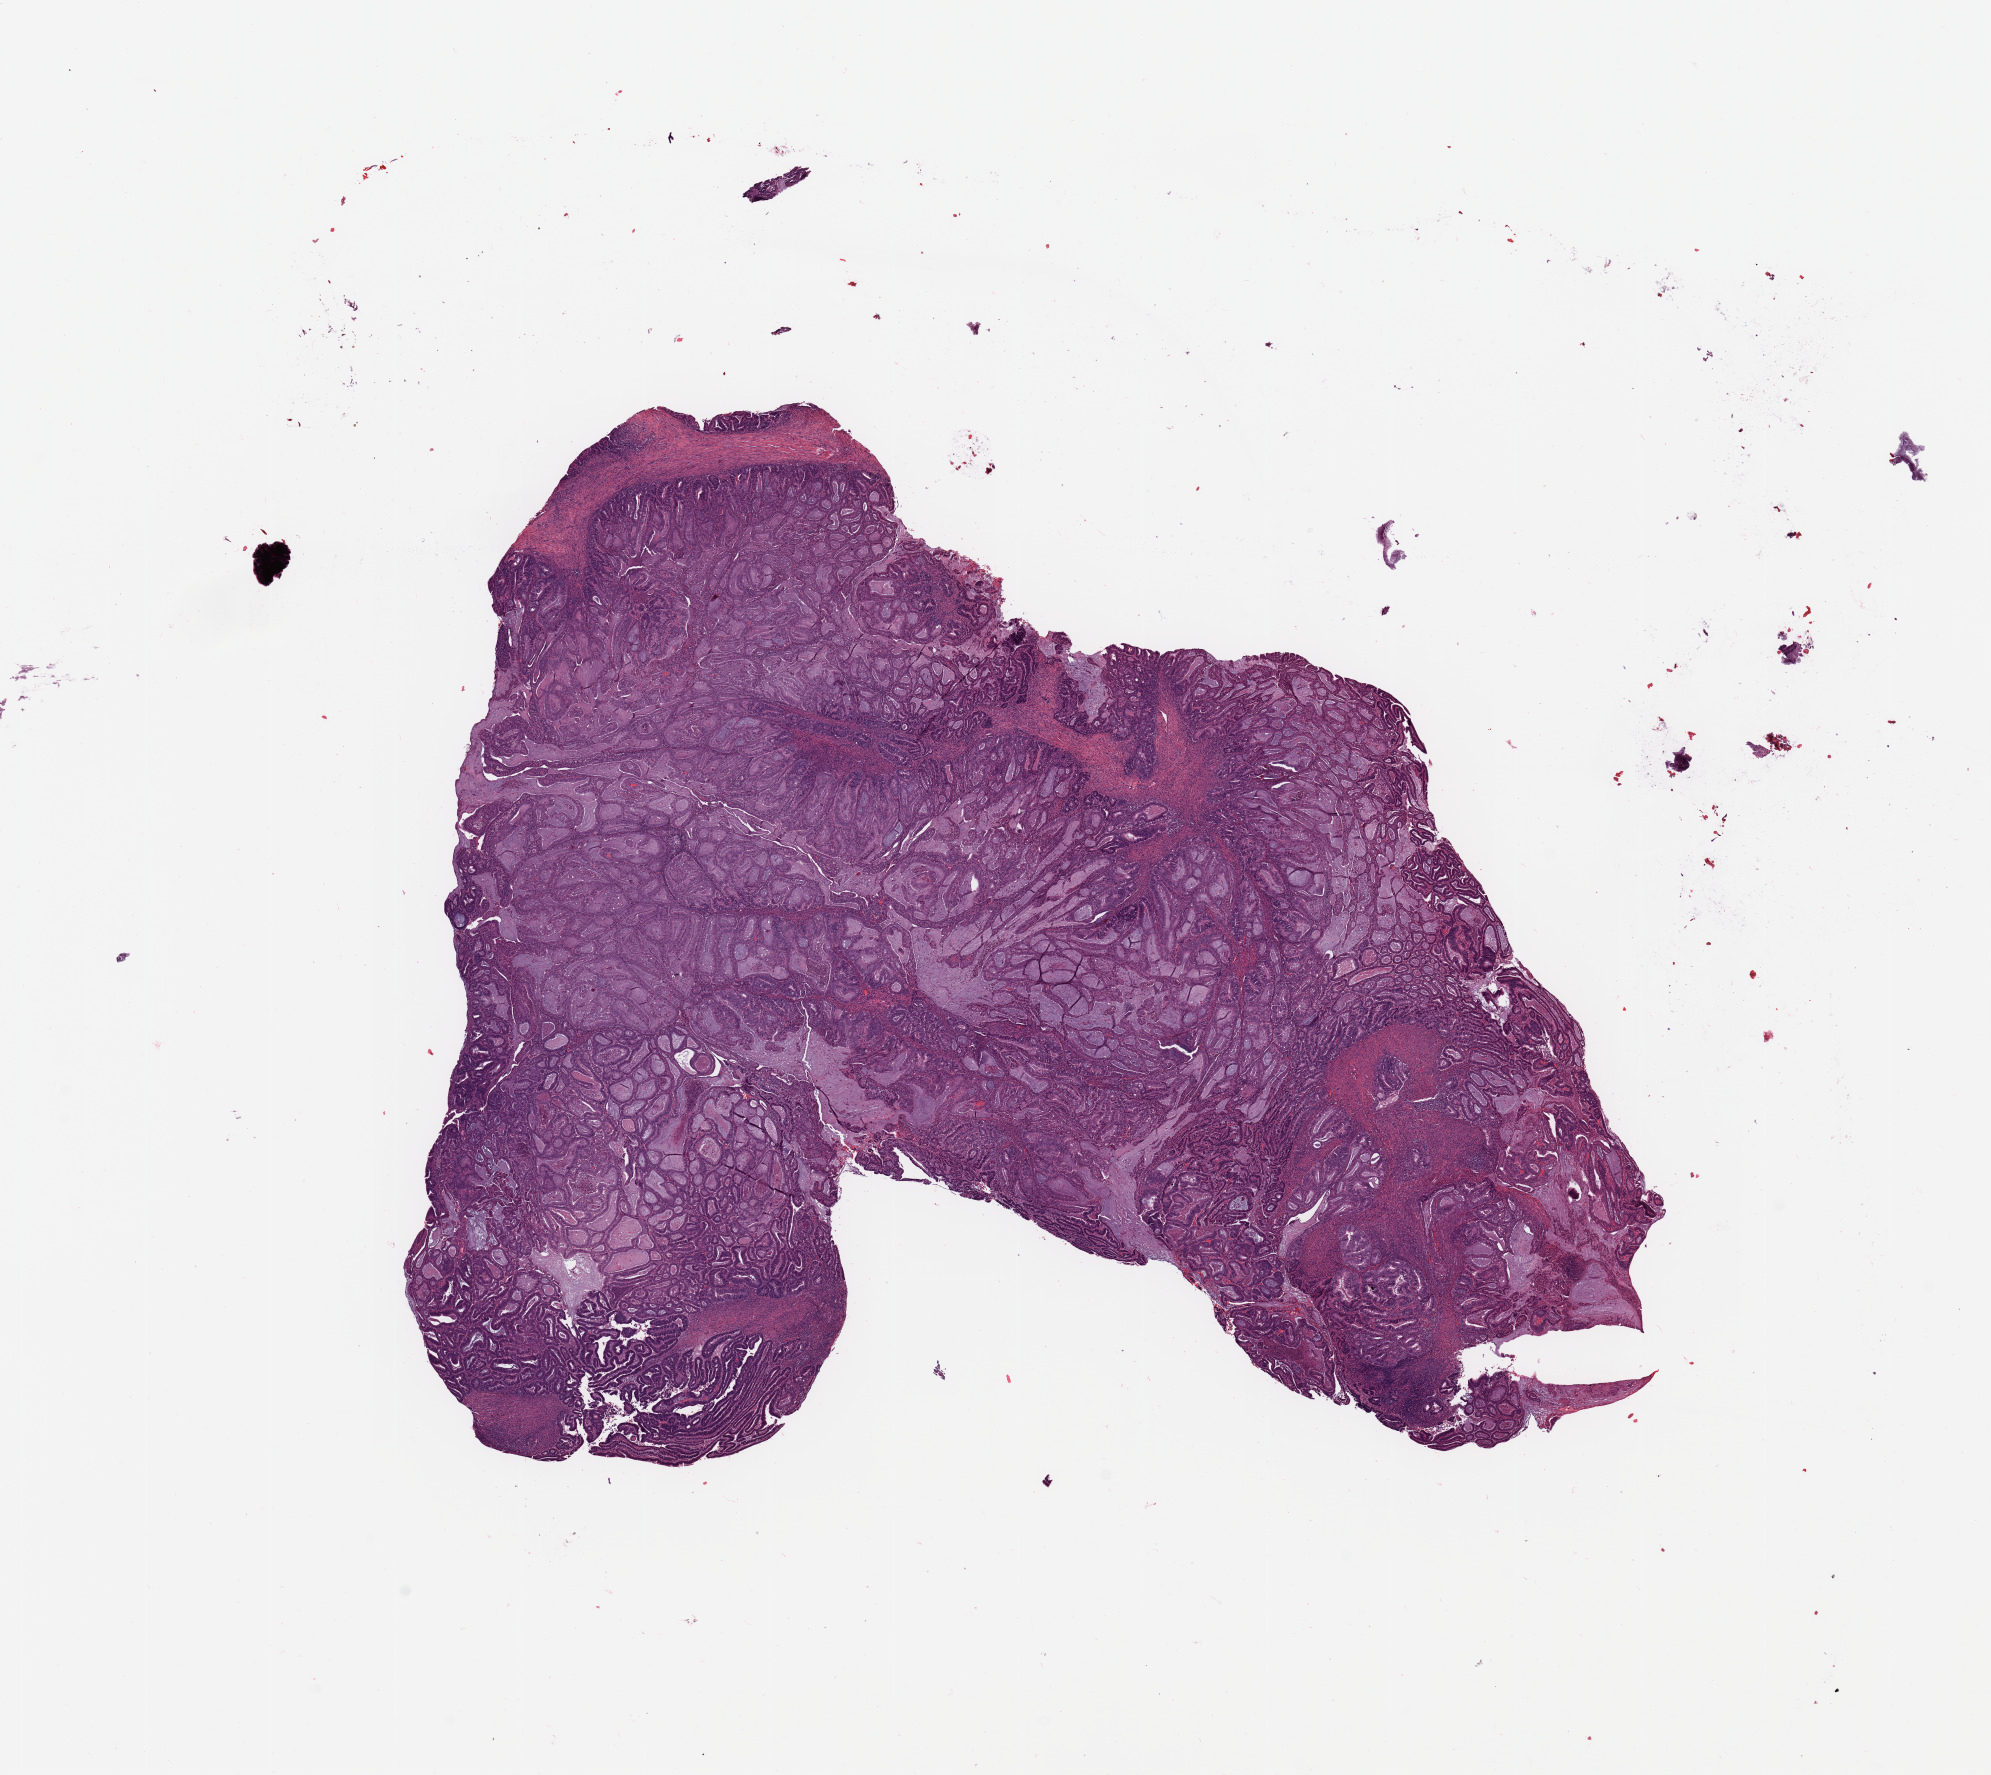
H&E-stained whole-slide image — whole scanned area (about 15.8 x 14.0 mm, from a 20x scan) shown as a low-resolution overview, tumour tissue sample, uterus. Female, 65 y/o. Histologic grade: G1 (well differentiated).
• diagnosis: Endometrioid adenocarcinoma, NOS
• AJCC pathologic stage: I